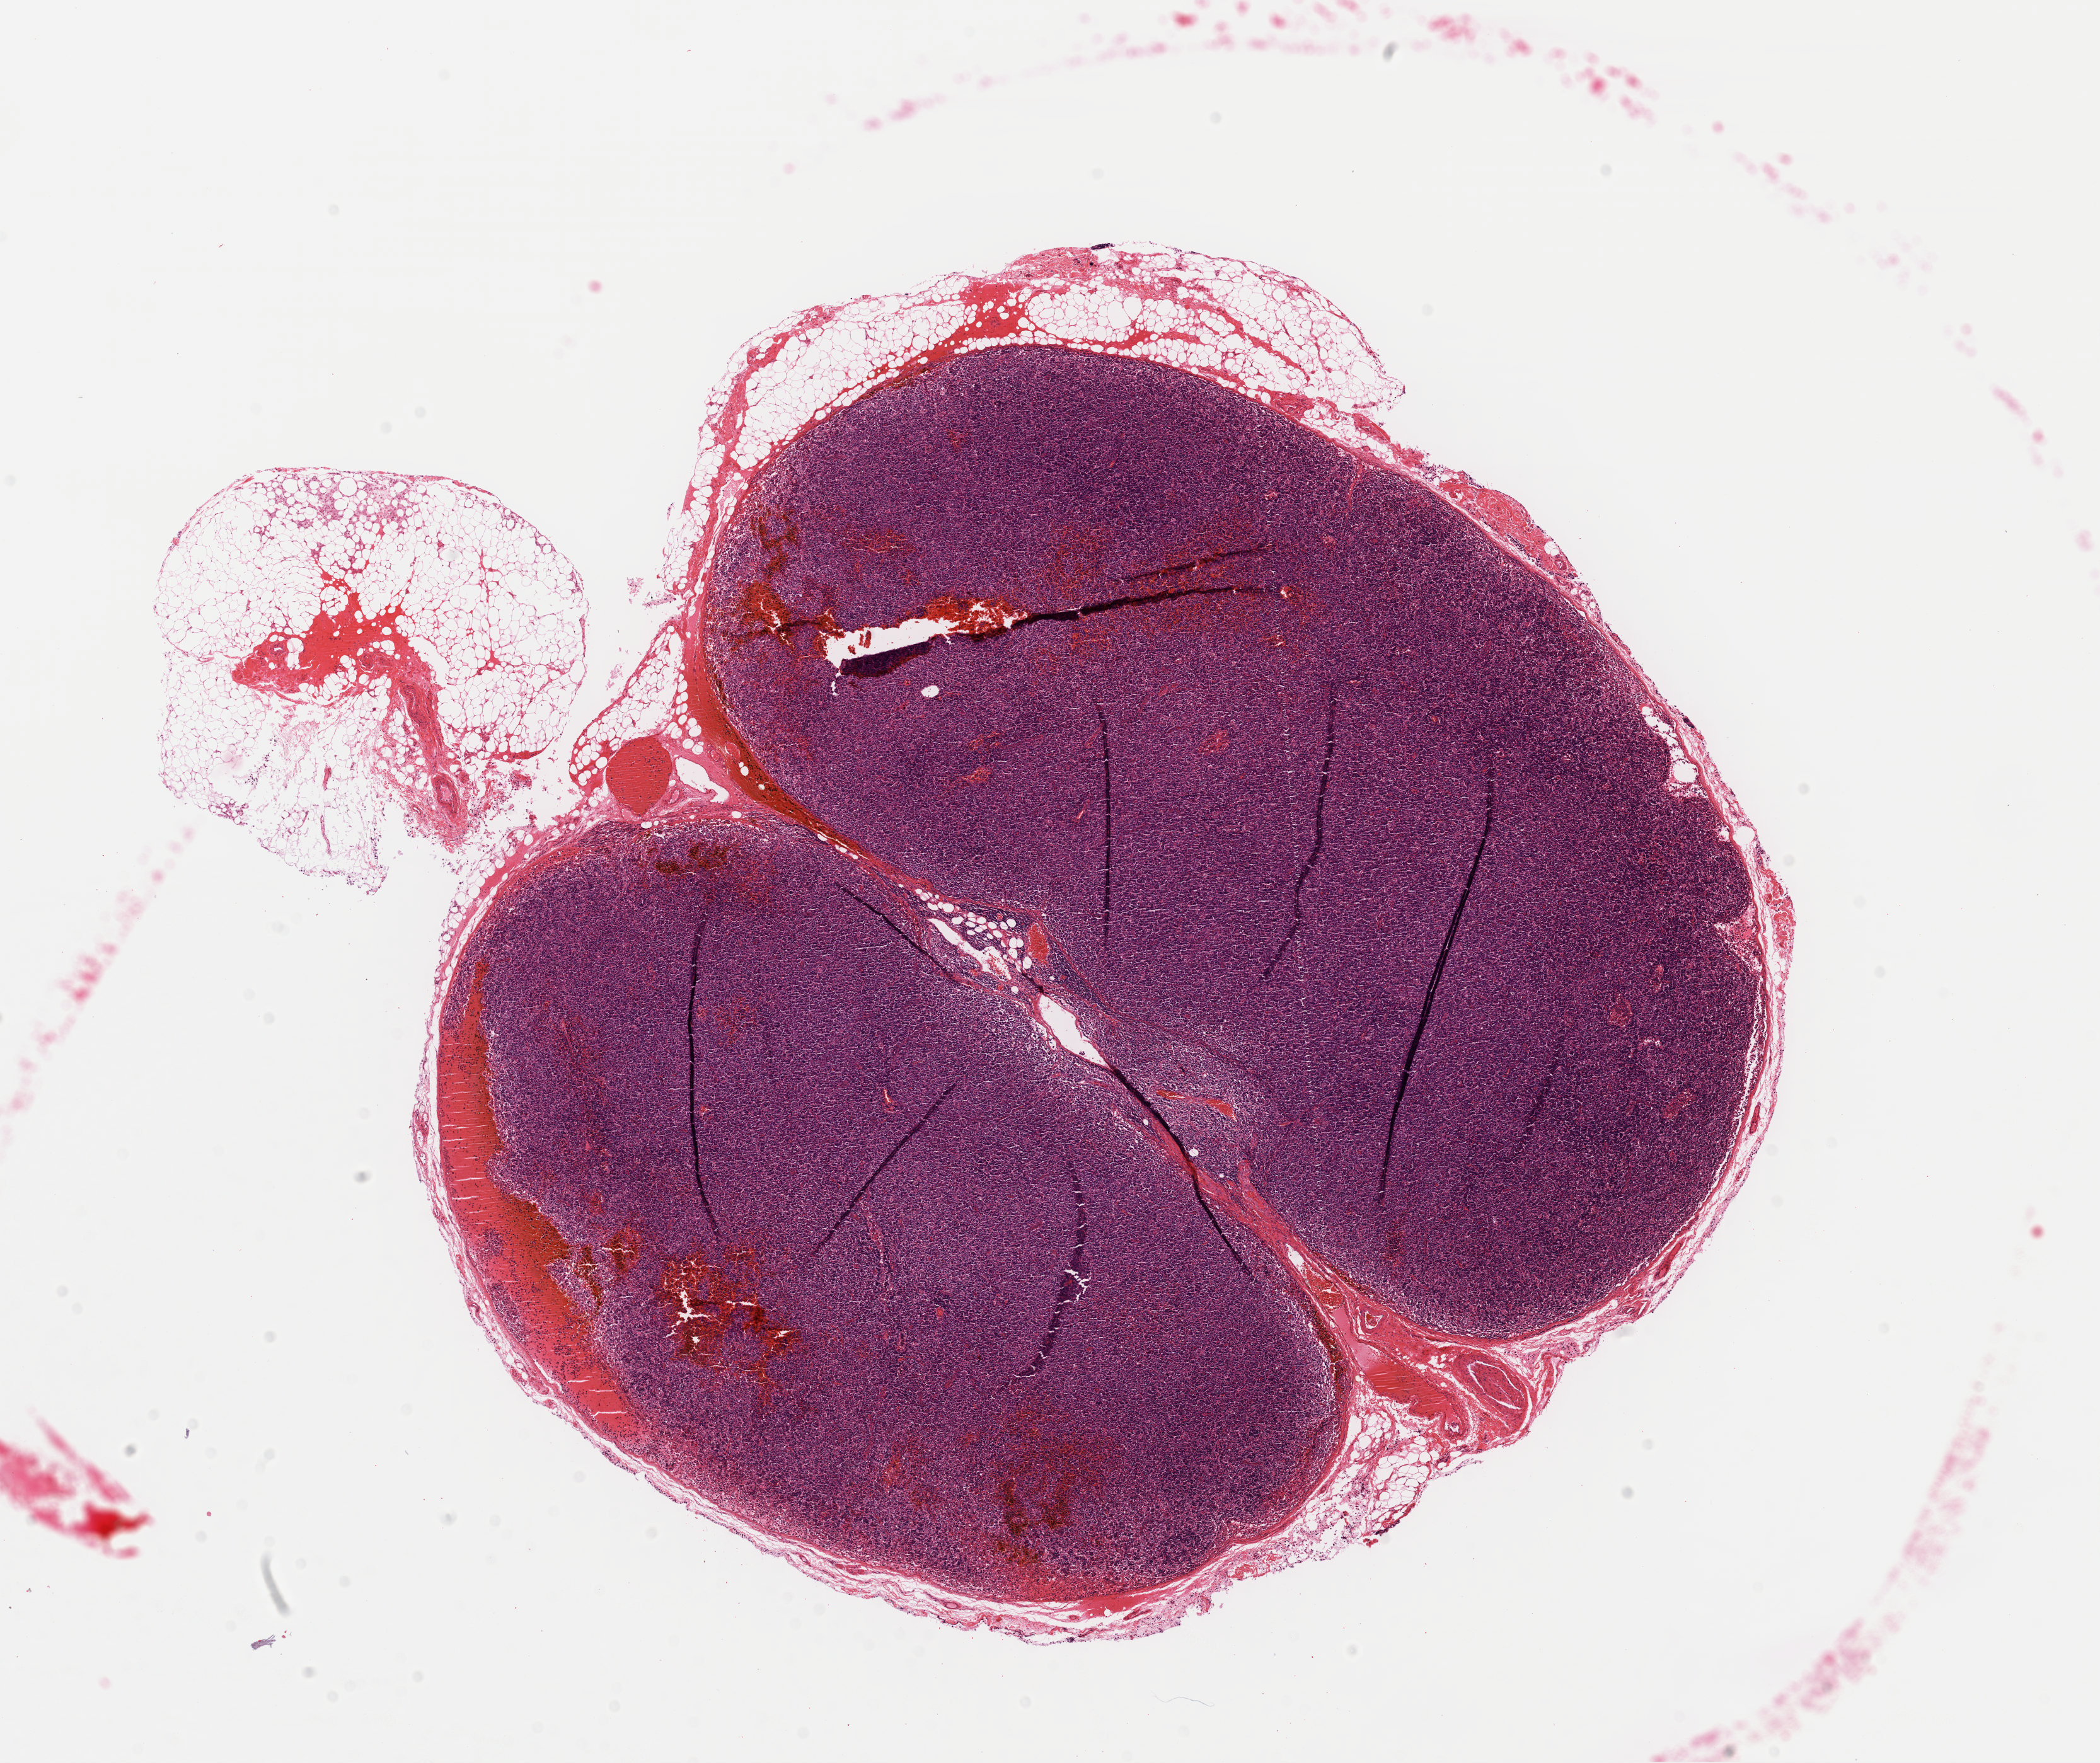
Whole-slide histology image, Hematoxylin and eosin (H&E) stained — whole scanned area (about 13.2 x 11.0 mm) shown as a low-resolution overview, formalin-fixed paraffin-embedded (FFPE) diagnostic section, primary tumour sample from the lymphoid tissue. Female patient; age at initial diagnosis 58 years.
Pathologic diagnosis: Diffuse large B-cell lymphoma, NOS (lymph nodes of head, face and neck).